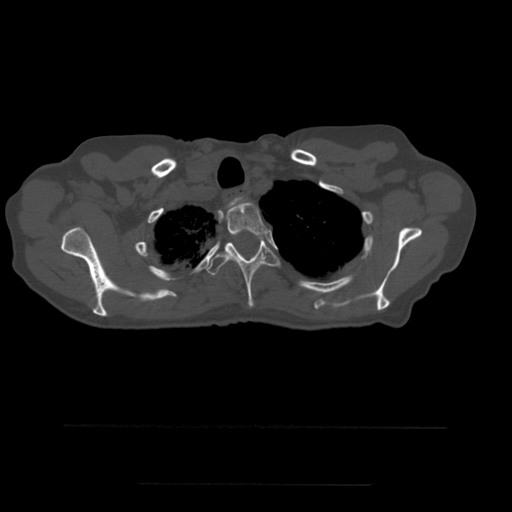
CT including the spine, one axial slice. Slice 427 of 544 in the series (ordered by position). Bone window (W 1800 / L 400 HU). 512 × 512 image matrix, field of view 350 × 350 mm. Patient age 58 years. From the clinical record (not read from this slice): primary cancer: lung.
Structures marked on this image (semi-automatic segmentation, software-assisted and operator-edited):
- T1 vertebra: bounding box <230,198,244,209> (left, top, right, bottom; pixels)
- T2 vertebra: <227,202,268,243>
- T3 vertebra: <207,235,280,308>